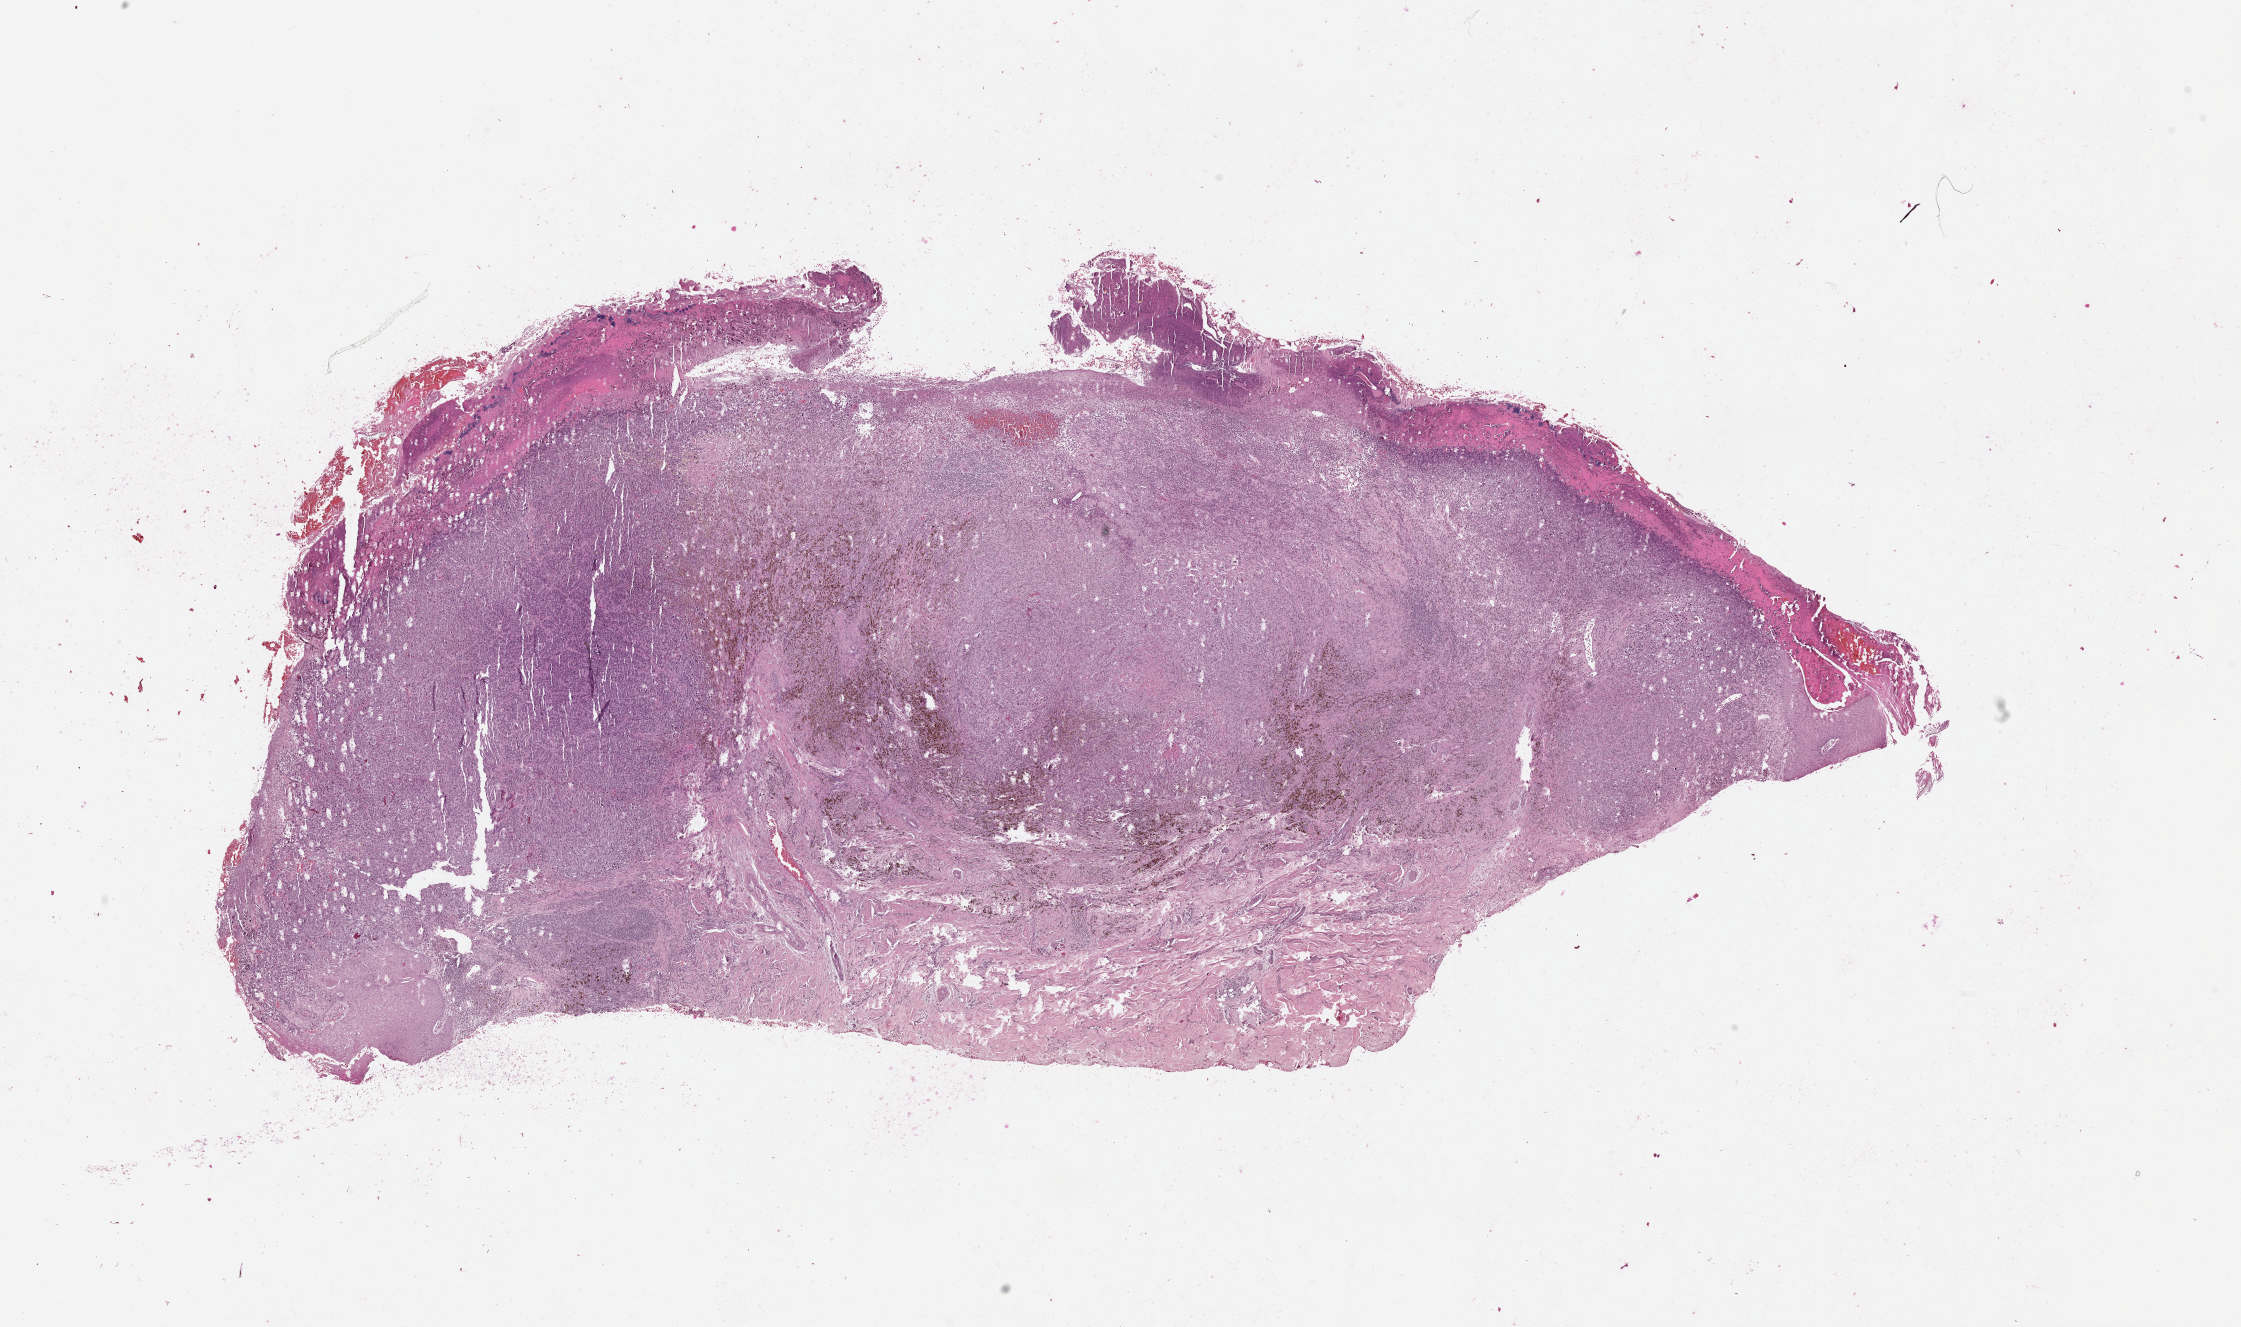
H&E-stained whole-slide image — shown as a low-resolution overview of the whole scanned area (about 18.0 x 10.7 mm, from a 20x scan), tumour tissue sample, sampled site: shoulder. Female, 68 y/o. Slide review estimates, as recorded: tumour nuclei 80%, necrosis 0%.
* diagnosis: Malignant melanoma, NOS
* AJCC pathologic stage: IIC